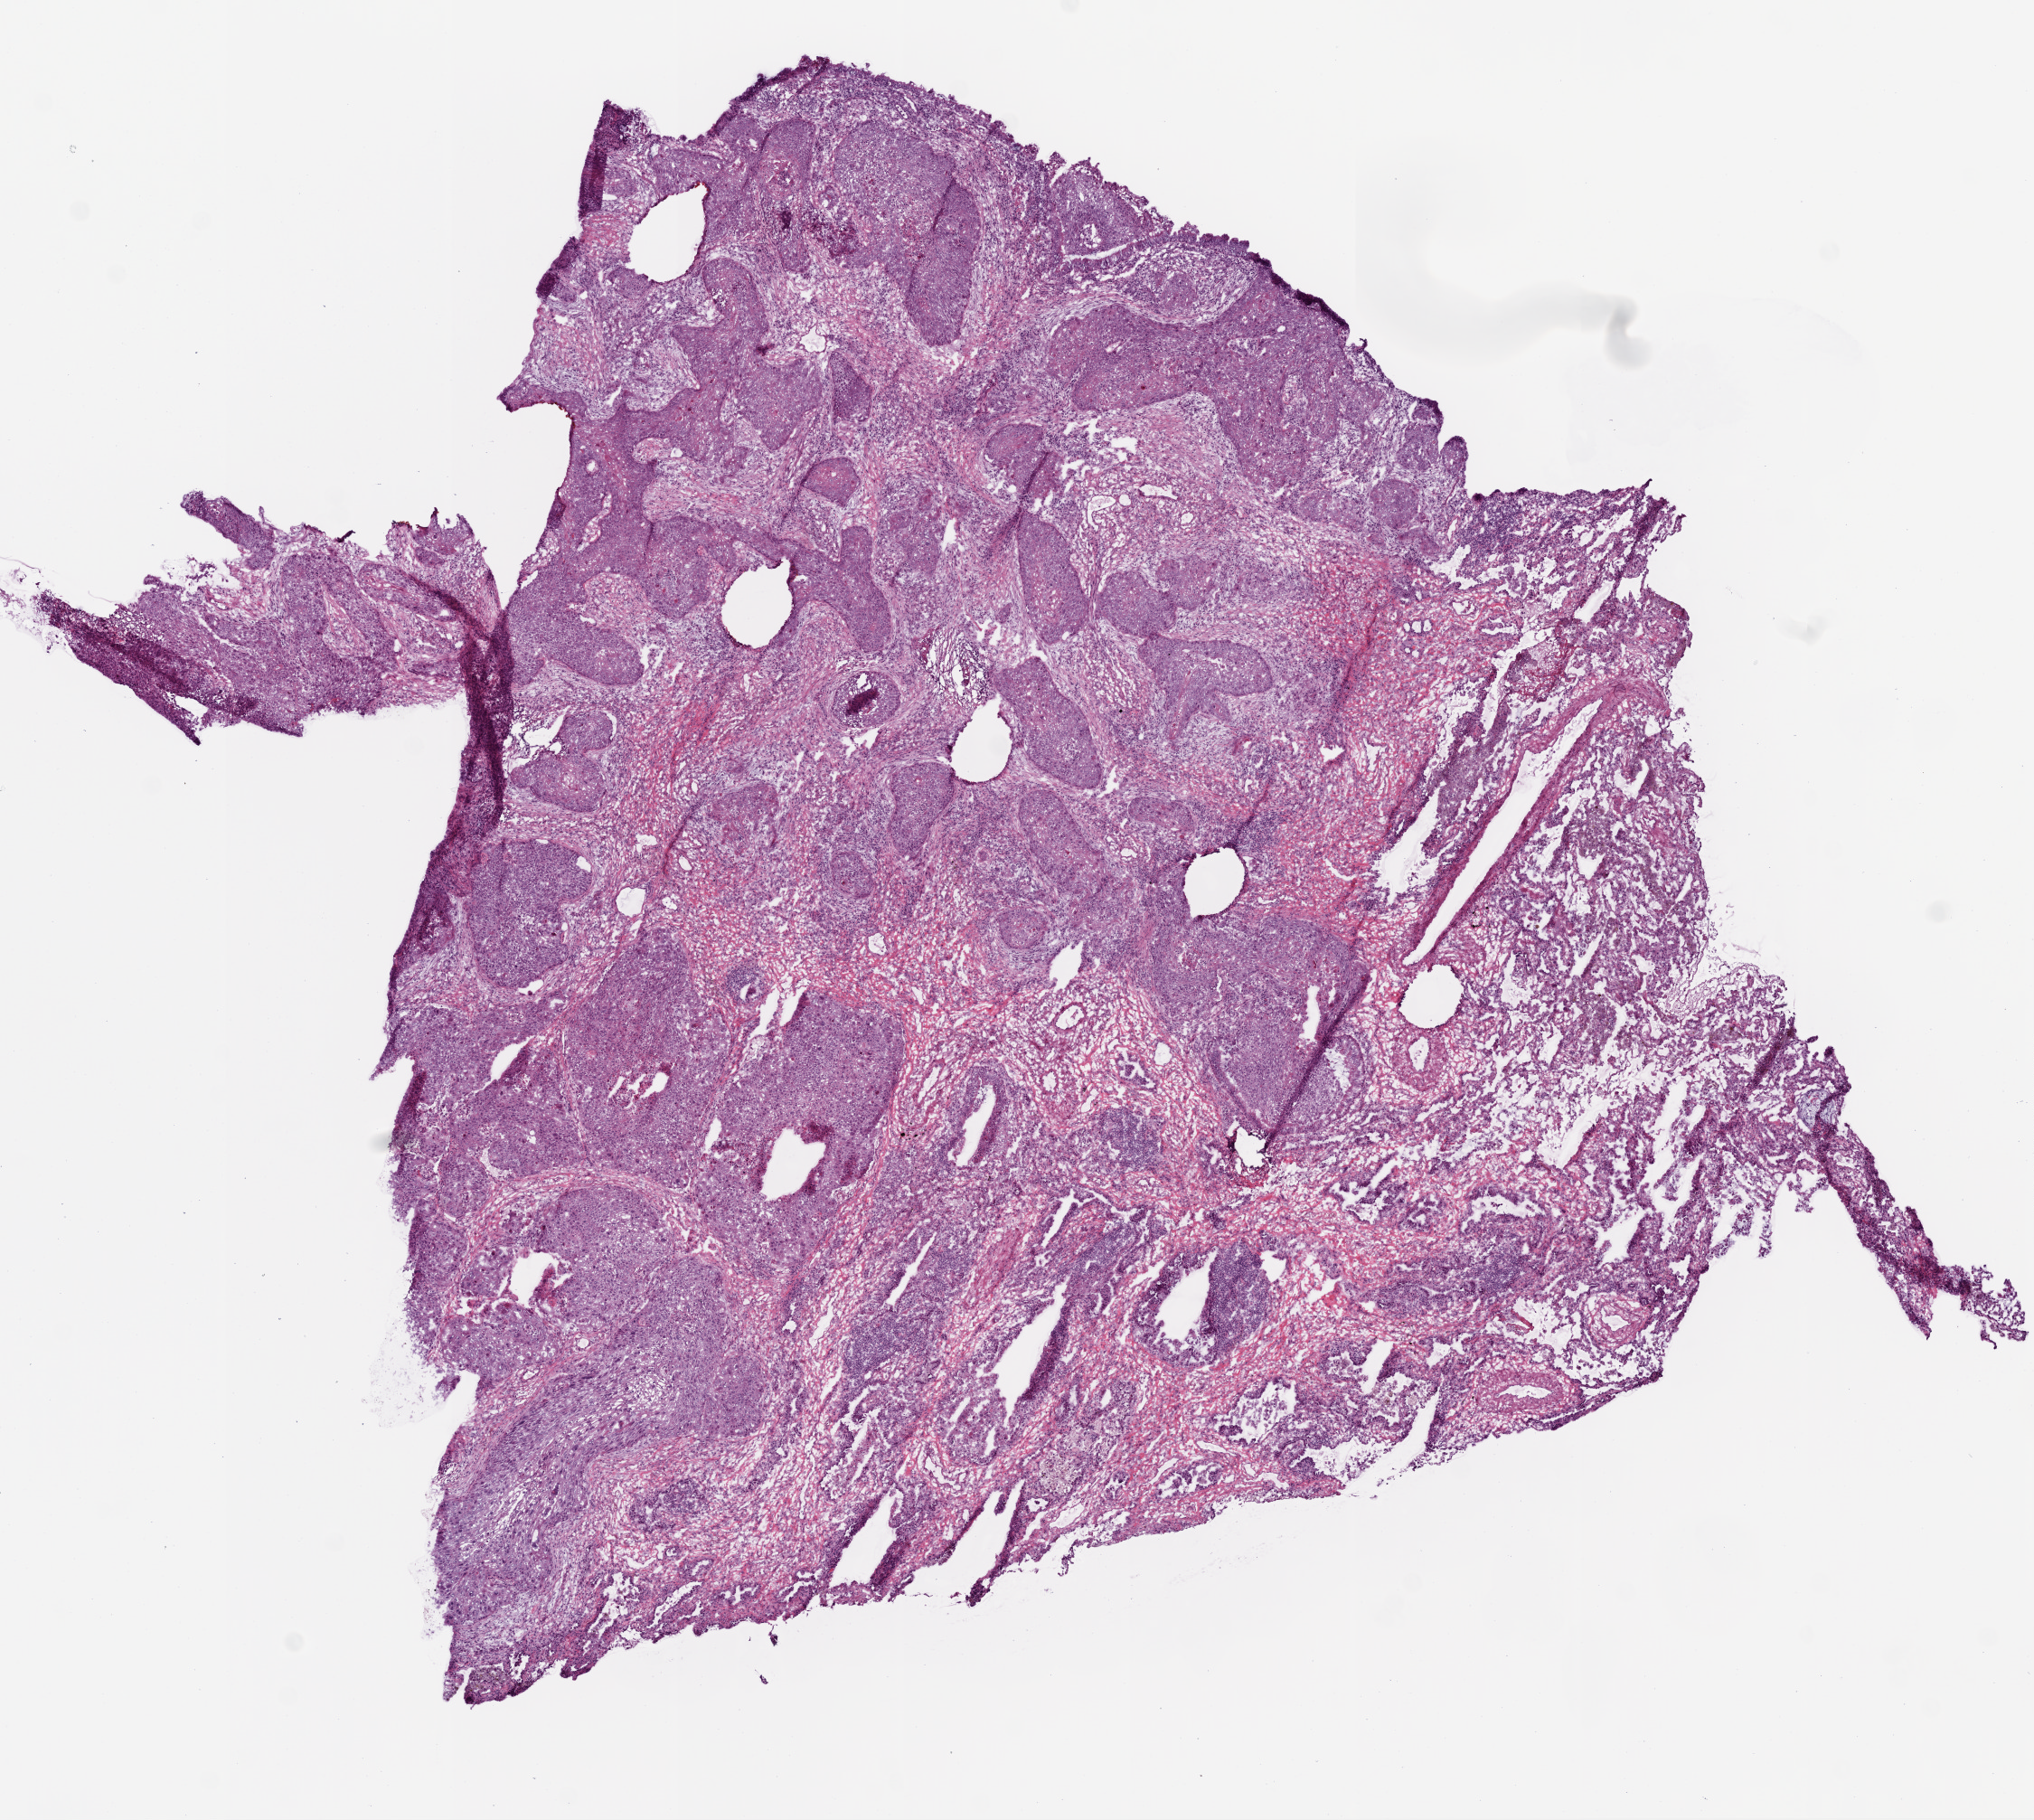
H&E-stained whole-slide image, whole scanned area (about 9.0 x 8.1 mm, acquisition: 20x scan) shown as a low-resolution overview; frozen section; sample: primary tumour, lung. Female, age 75 years at initial diagnosis. Composition of this section per pathologist review: tumour cells 100%, tumour nuclei 70%, normal cells 0%, stromal cells 0%, necrosis 0%. Infiltration values recorded for this section: lymphocyte infiltration 10%, monocyte infiltration 8%, neutrophil infiltration 10%.
• AJCC pathologic stage: IIA (7th edition)
• pathologic diagnosis: Squamous cell carcinoma, NOS (lower lobe, lung)